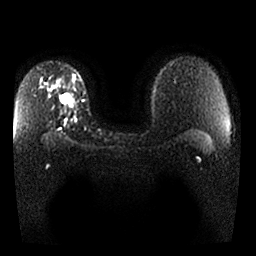
Breast MRI, one axial slice. Slice 19 of 25 in the series (ordered by position). Diffusion-weighted series; image 2 of 4 stored at this slice position (different b-values; order by instance number). 1.5 T. 4 mm slice thickness. 256 × 256 image matrix. Female patient.
Structures marked on this image (expert manual segmentation):
- tumour on diffusion-weighted imaging: bounding box <59,91,72,104> (left, top, right, bottom; pixels)